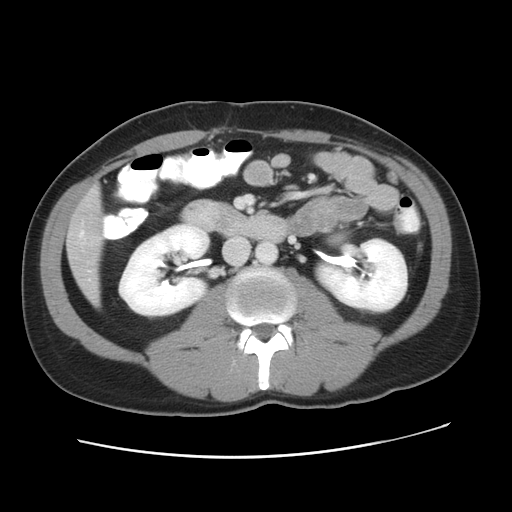
Contrast-enhanced abdominal CT, one axial slice. Slice 17 of 49 in the series (ordered by position). 120 kVp. Intravenous contrast given. Soft-tissue window (W 400 / L 40 HU). 5 mm slice thickness. 512 × 512 image matrix. Male patient, age 41 years. From the clinical record (not read from this slice): diagnosis: colorectal cancer liver metastases, imaged before liver resection; multiple liver metastases: yes; largest metastasis: 0.7 cm; chemotherapy before resection: yes.
Structures marked on this image (expert manual segmentation):
- hepatic veins: bounding box [x1, y1, x2, y2] px = [79, 231, 84, 235]
- liver: [68, 191, 102, 299]